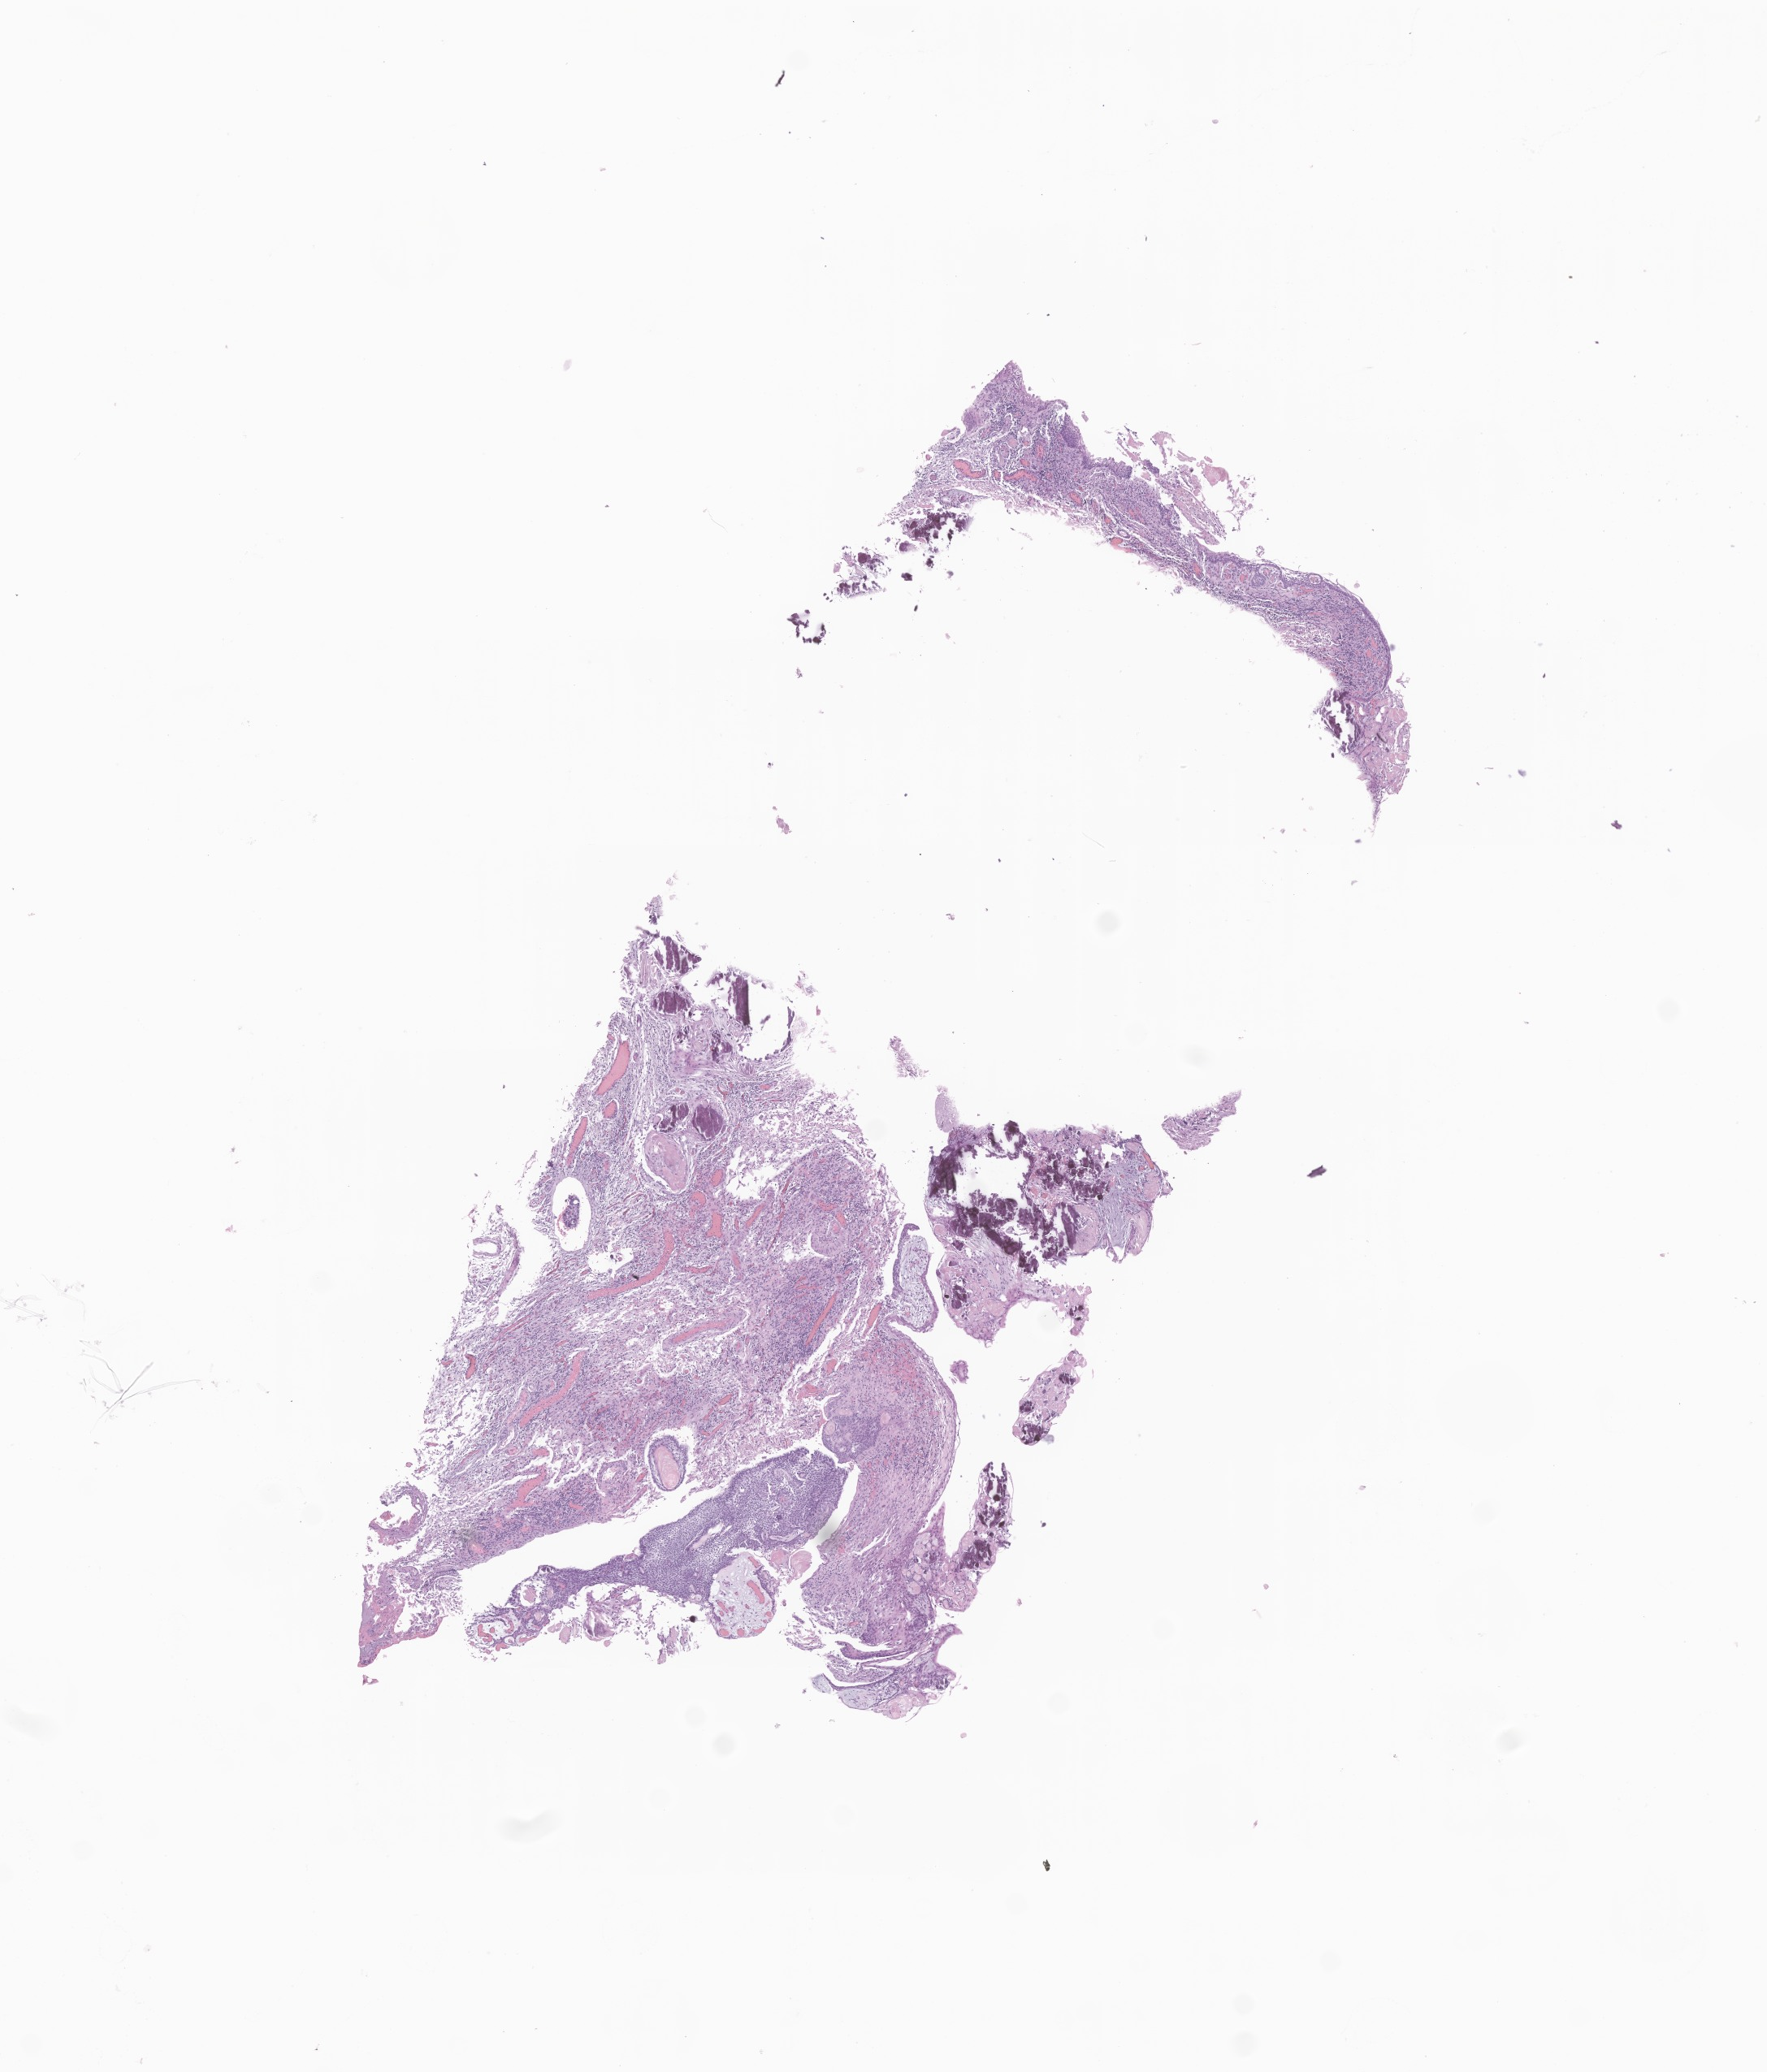
Whole-slide image, H&E stain of tumor tissue from the brain — low-resolution overview of the scanned area, about 9.2 x 10.8 mm, formalin-fixed paraffin-embedded section. Patient female; age 159 months.
- diagnosis (ICD-O-3 morphology term): Craniopharyngioma, NOS